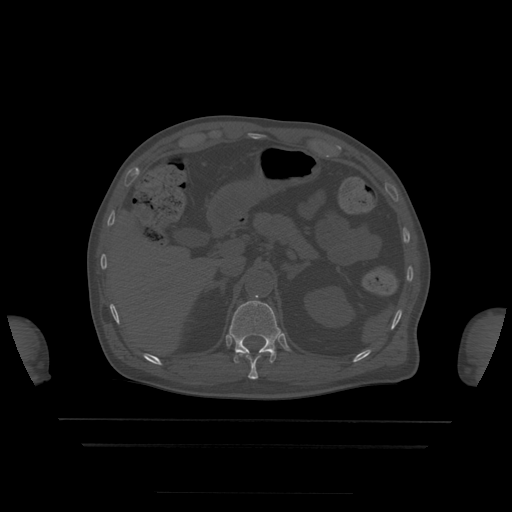
CT including the spine, one axial slice. Position 204 of 522 along the scan axis. Bone window (W 1800 / L 400 HU). 512 × 512 image matrix, field of view 436 × 436 mm. Patient age 68 years. Case-level facts recorded for this patient, not image findings: primary cancer: urothelial.
Outlined on this slice (semi-automatic segmentation, software-assisted and operator-edited):
- T11 vertebra: box from (x=240, y=352) to (x=274, y=380) px
- T12 vertebra: (x=229, y=295)–(x=281, y=364)